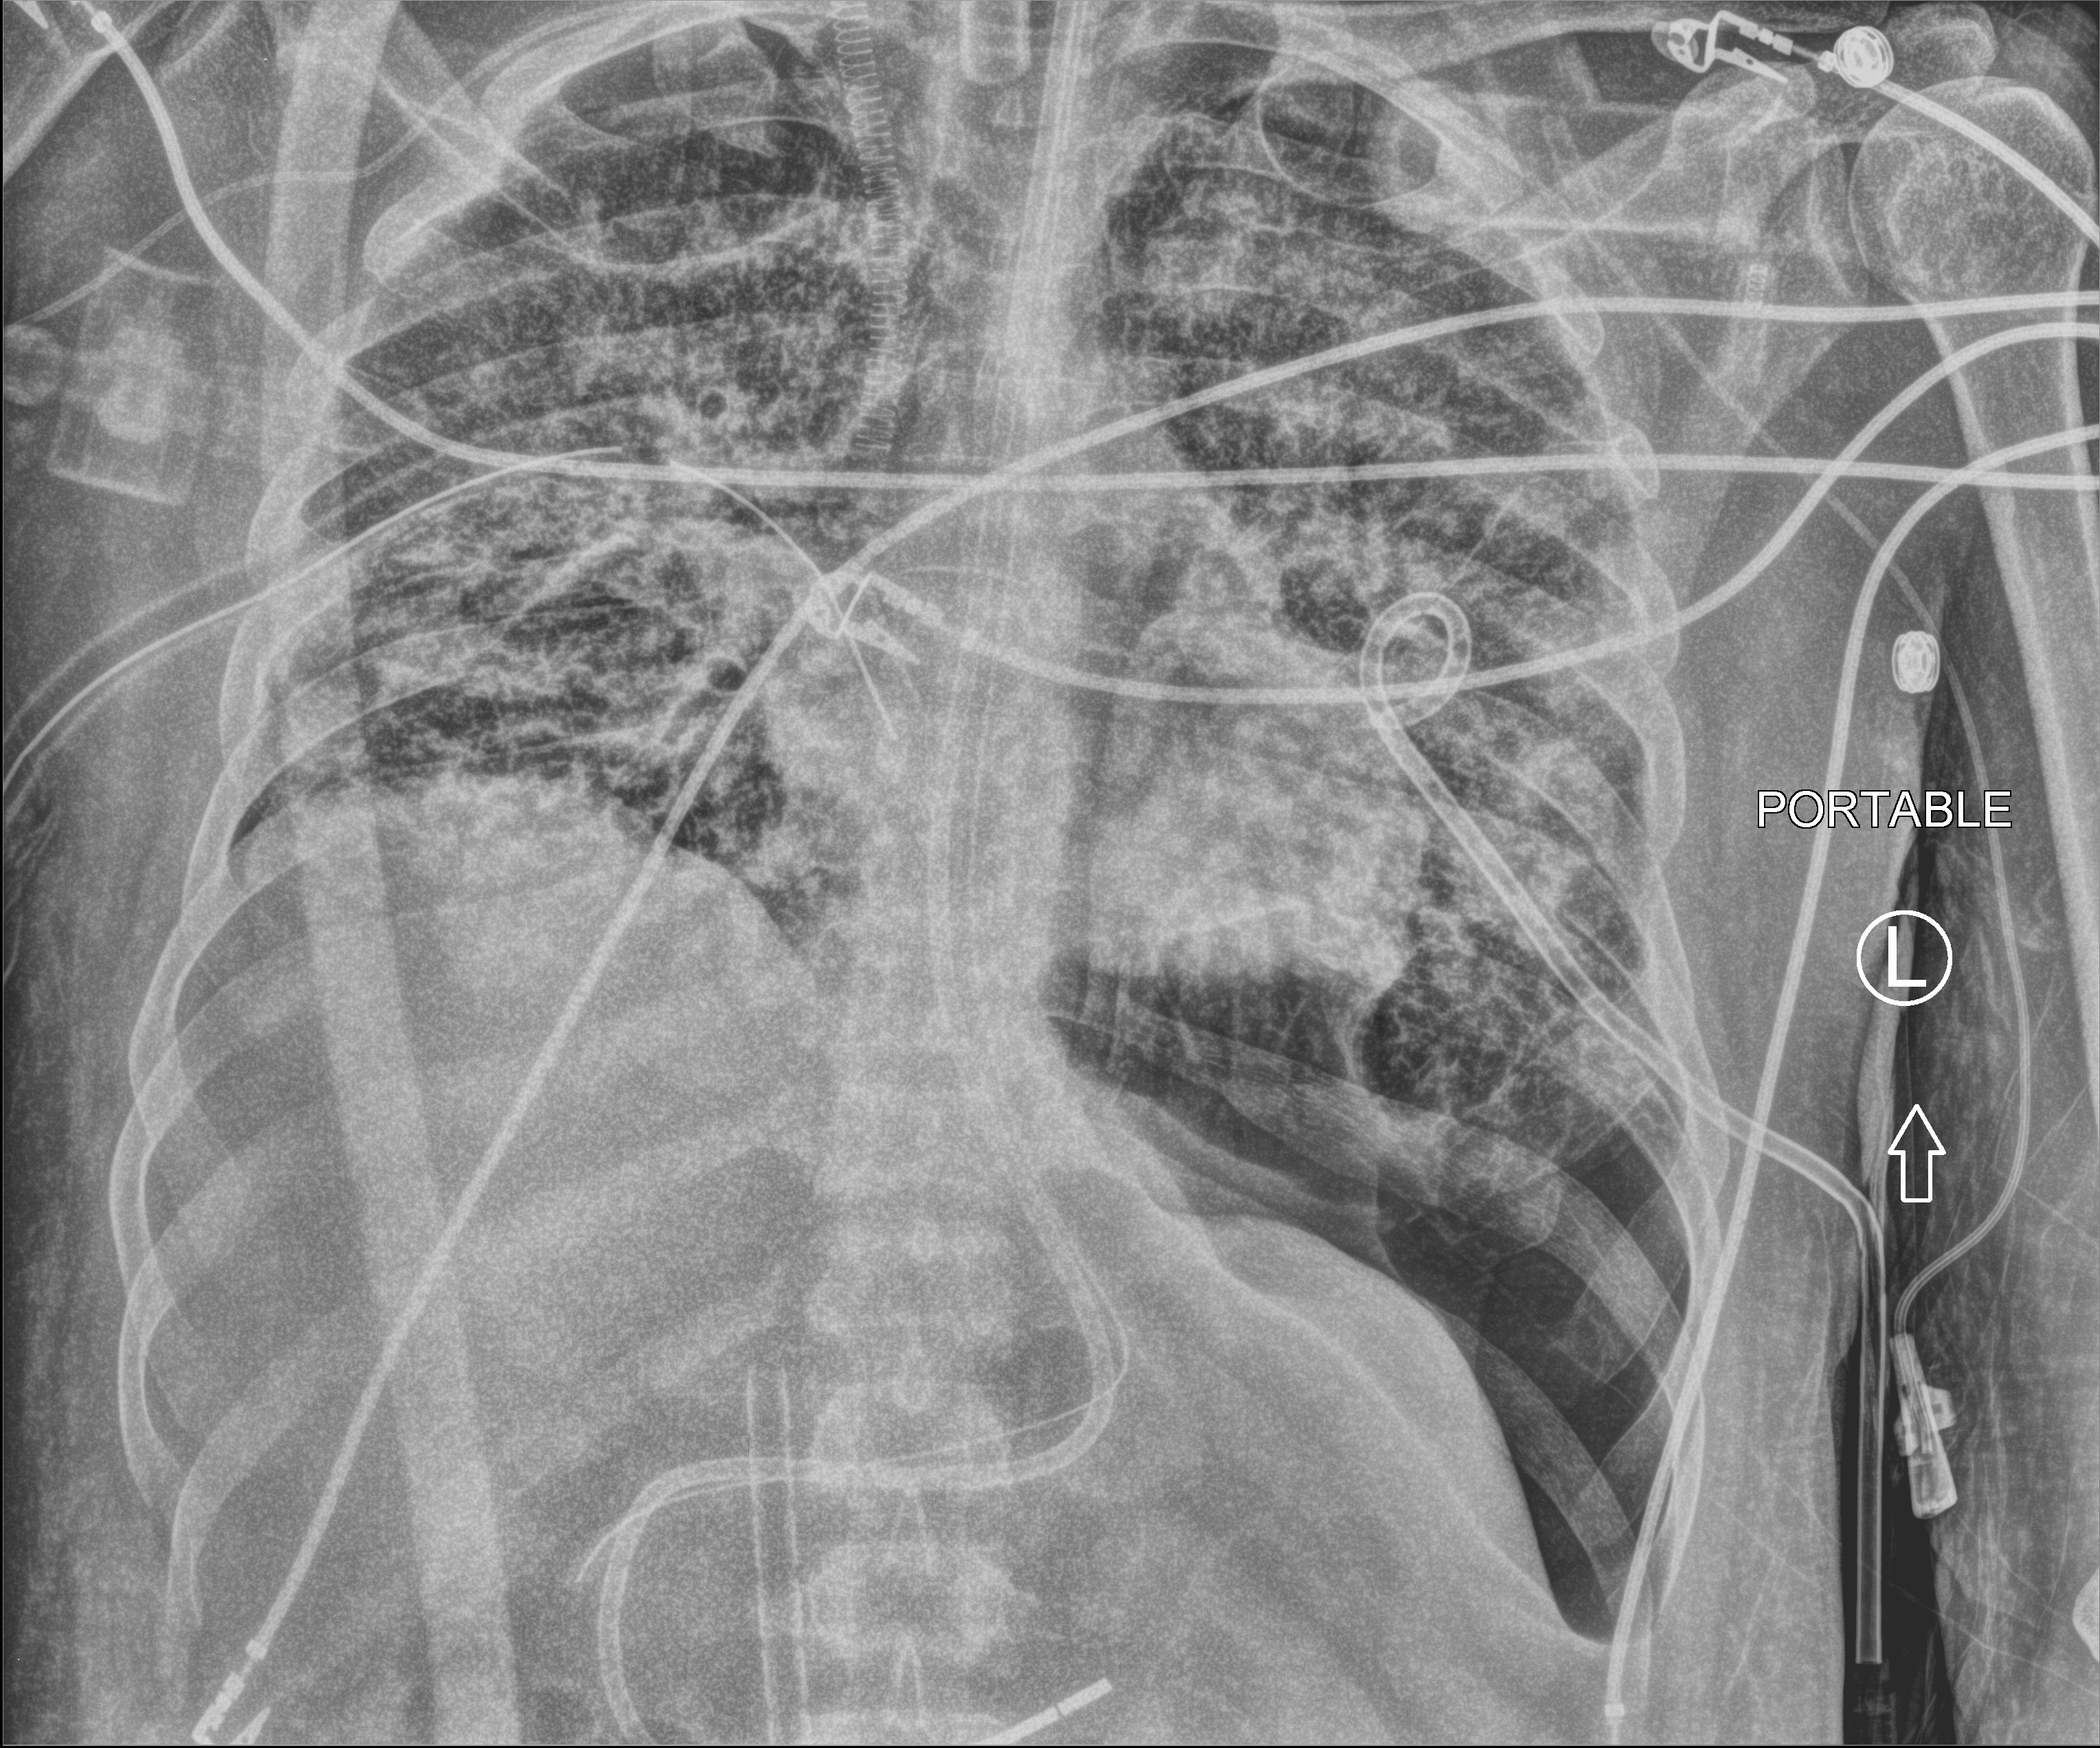
Bedside chest radiograph (computed radiography). Patient hospitalised with COVID-19, aged 18–59 years.
Hospital-stay facts (about this admission, not read from this image; timing relative to this image not recorded): mechanically ventilated during this hospital stay: yes.